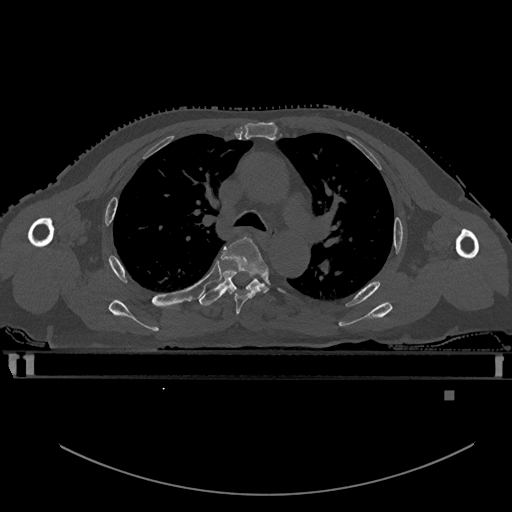
CT including the spine, one axial slice; slice 384 of 969 in the series (ordered by position); bone window (W 1800 / L 400 HU); 0.5 mm slice thickness; 512 × 512 image matrix, field of view 456 × 456 mm. Patient: male, 82 years. From the clinical record (not read from this slice): primary cancer: prostate; vertebrae with lytic lesions (as recorded): T11, T9, T8, T2.
Annotated regions visible in this slice (semi-automatic segmentation, software-assisted and operator-edited):
- T4 vertebra: bounding box (x1, y1, x2, y2) in pixels: (221, 236, 269, 314)
- T5 vertebra: (199, 270, 272, 306)